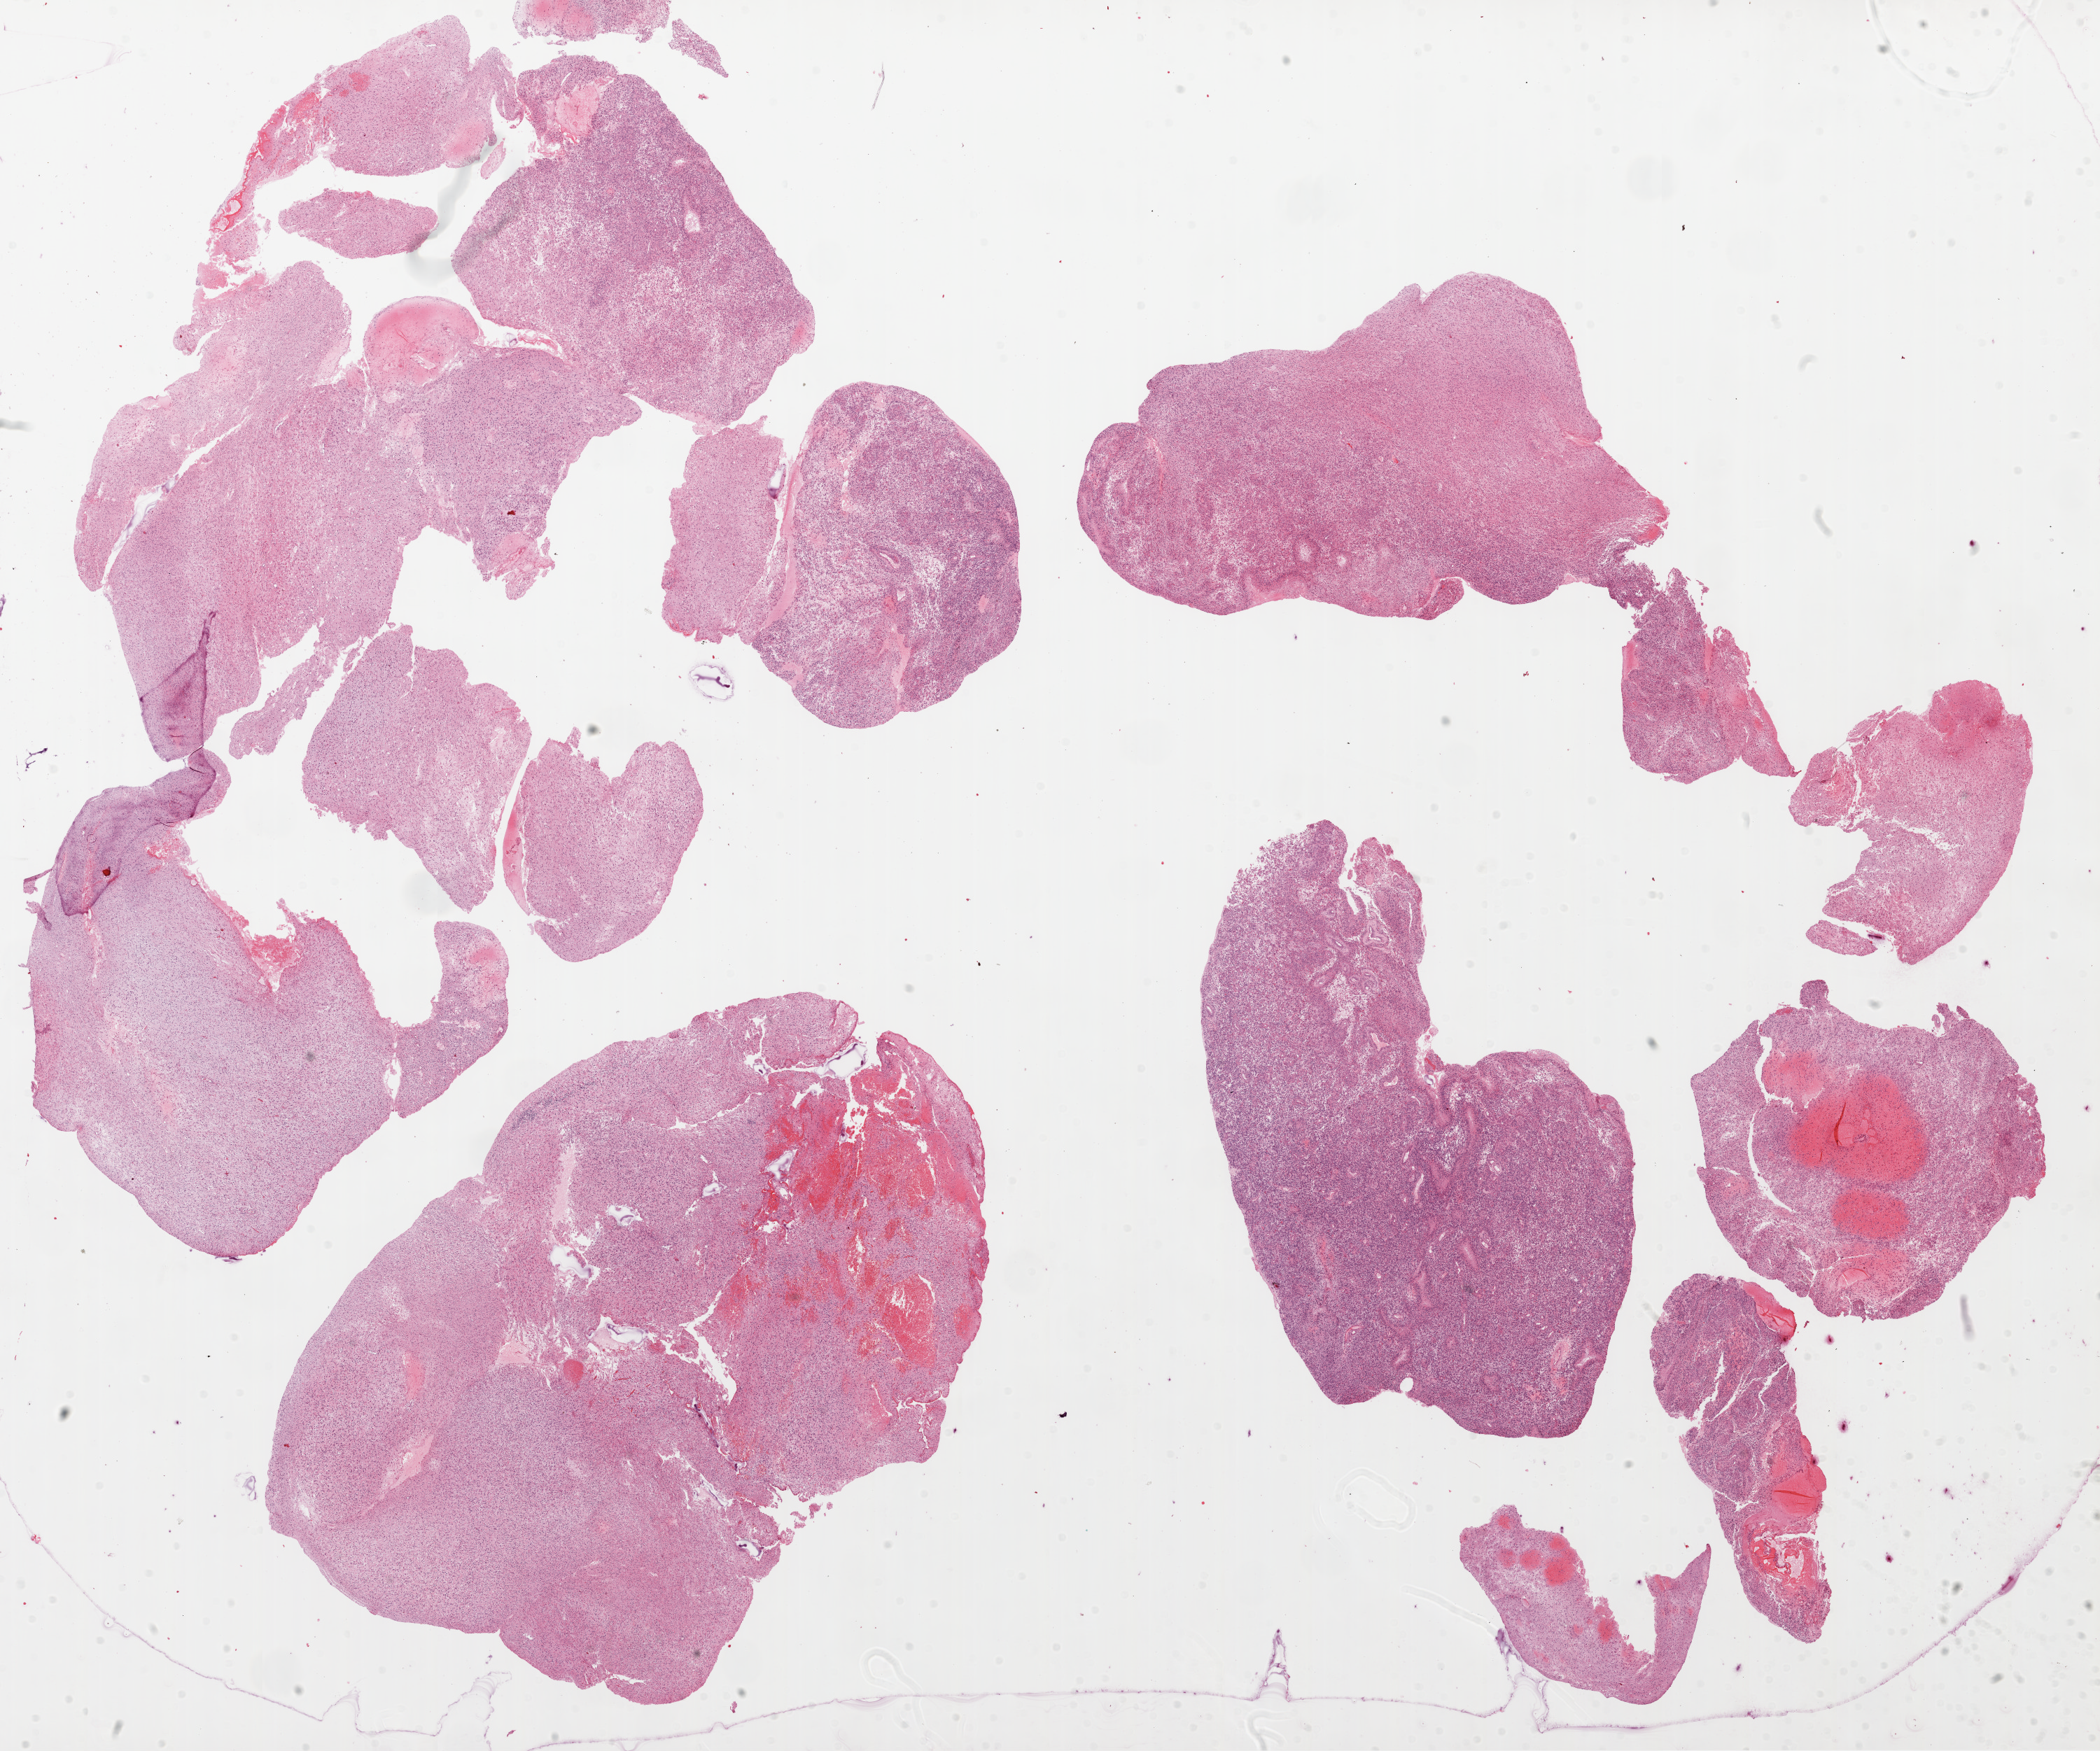
Hematoxylin and eosin (H&E) stained whole-slide image, shown as a low-resolution overview of the whole scanned area (about 24.1 x 20.1 mm). FFPE section. Primary tumour sample from the brain. Male, age 56 years at initial diagnosis.
- diagnosis: Glioblastoma